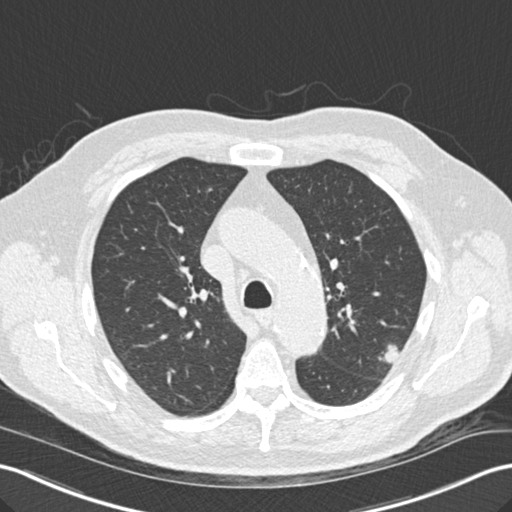
Low-dose screening chest CT, one axial slice. Slice 107 of 157 in the series (ordered by position). Reconstruction kernel B30f. 120 kVp. Lung window (W 1500 / L -600 HU). 2 mm slice thickness. 512 × 512 image matrix, field of view 354 × 354 mm.
Structures marked on this image (outlined manually by an expert reader):
- lesion 1 (tumor, upper lobe of left lung): bounding box <379,345,398,363> (left, top, right, bottom; pixels)